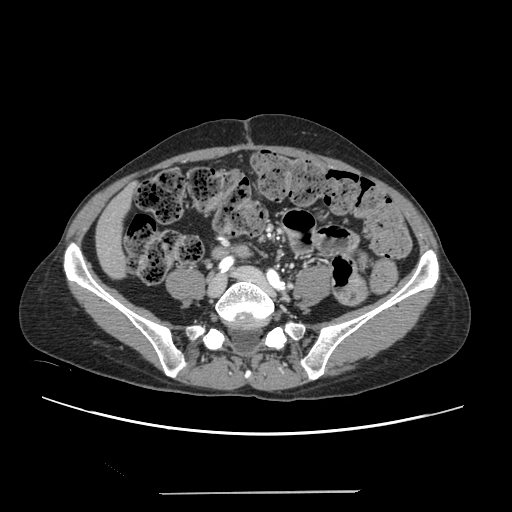
Contrast-enhanced abdominal CT, one axial slice. Position 20 of 240 along the scan axis. Intravenous contrast given. Soft-tissue window (W 400 / L 40 HU). 512 × 512 image matrix. Female patient, age 60 years. From the clinical record (not read from this slice): diagnosis: colorectal cancer liver metastases, imaged before liver resection; multiple liver metastases: no; largest metastasis: 1.5 cm; disease in both lobes: no.
Structures marked on this image (manually delineated by an expert):
- liver: bounding box <97,189,133,277> (left, top, right, bottom; pixels)
- planned liver remnant (the part of the liver to remain after resection): <97,189,133,277>